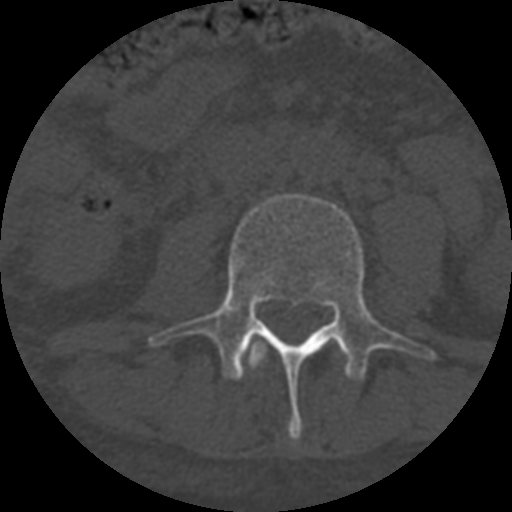
CT including the spine, one axial slice. Position 238 of 708 along the scan axis. Reconstruction kernel STANDARD. One of 3 acquisitions stored at this slice position. Bone window (W 1800 / L 400 HU). 1.25 mm slice thickness. 512 × 512 image matrix. Patient age 55 years. Case-level facts recorded for this patient, not image findings: primary cancer: colon.
Structures marked on this image (semi-automatically segmented with operator editing):
- L2 vertebra: box from (x=248, y=341) to (x=268, y=370) px
- L3 vertebra: (x=148, y=193)–(x=437, y=439)